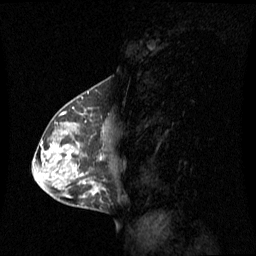
Breast MRI (dynamic contrast-enhanced), one sagittal slice; position 35 of 60 along the scan axis; dynamic contrast-enhanced series, image 2 of 3 at this slice position (ordered by acquisition); 1.5 T; TE 4.2 ms, TR 8.4 ms; 2 mm slice thickness; 256 × 256 image matrix, field of view 270 × 270 mm. Patient: female, 42 years. Case-level facts recorded for this patient, not image findings: setting: breast cancer imaged before/during neoadjuvant chemotherapy; receptor status: HR-positive, HER2-negative.
Structures marked on this image (semi-automatic segmentation, software-assisted and operator-edited):
- analysis volume of interest (the breast-tissue region the enhancement analysis was run in; not a lesion): bounding box [x1, y1, x2, y2] px = [56, 113, 109, 185]
- tumour enhancement mask (voxels above the 70 % enhancement threshold inside the analysis volume of interest): [61, 148, 102, 160]